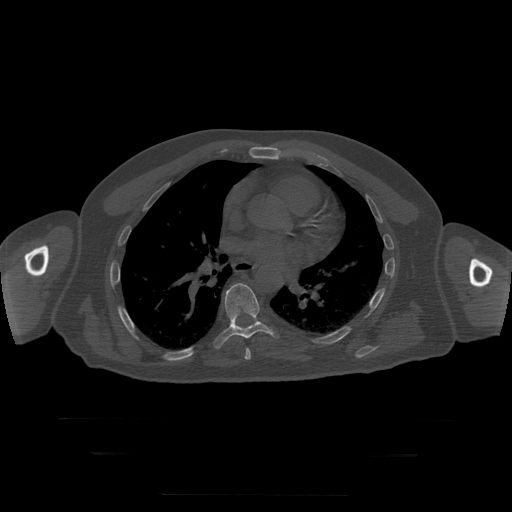
CT including the spine, one axial slice. Slice 168 of 397 in the series (ordered by position). Reconstruction kernel STANDARD. 120 kVp. Bone window (W 1800 / L 400 HU). 1.25 mm slice thickness. 512 × 512 image matrix, field of view 510 × 510 mm. Patient age 73 years. Case-level facts recorded for this patient, not image findings: primary cancer: prostate.
Annotated regions visible in this slice (semi-automatically segmented with operator editing):
- T7 vertebra: bounding box <245,349,251,360> (left, top, right, bottom; pixels)
- T8 vertebra: <214,283,279,349>